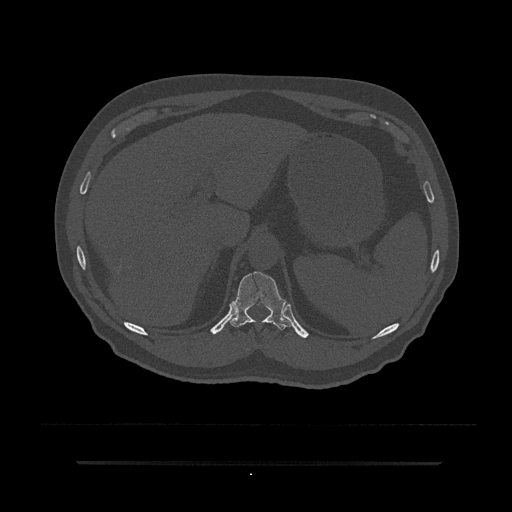
CT including the spine, one axial slice. Slice 276 of 797 in the series (ordered by position). Reconstruction kernel Br40s/3. 120 kVp. Bone window (W 1800 / L 400 HU). 512 × 512 image matrix, field of view 464 × 464 mm. Patient: male, 59 years. Case-level facts recorded for this patient, not image findings: primary cancer: bile ducts; vertebrae with lytic lesions (as recorded): T10.
Annotated regions visible in this slice (semi-automatic segmentation, software-assisted and operator-edited):
- T11 vertebra: bounding box <230,271,294,330> (left, top, right, bottom; pixels)